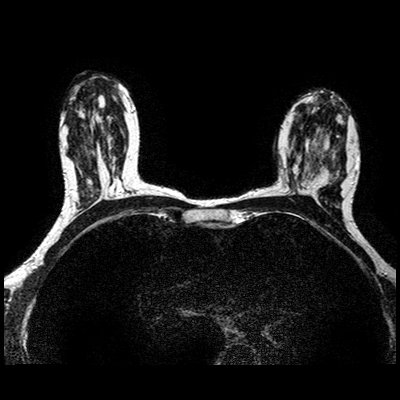
Breast MRI examination; 2 images, each one mid-volume slice chosen by position.
Image 1: axial T2-weighted / STIR image, slice 43 of 84.
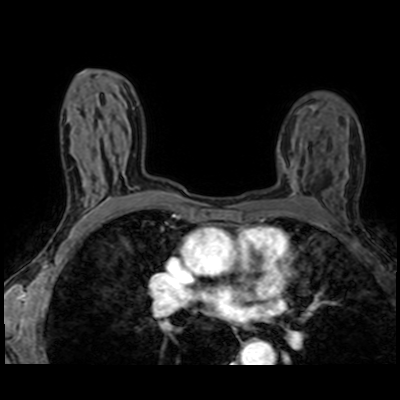
Image 2: post-contrast dynamic axial slice, series "AX BLISS_AUTO SENSE", slice 43 of 84, dynamic phase 5 of 8.
Patient-level pathology facts (from the clinical record, not from the images): pathology diagnosis: ducta CA in situ (left breast); receptor status (as recorded): ER neg, PR neg, HER2 pos.